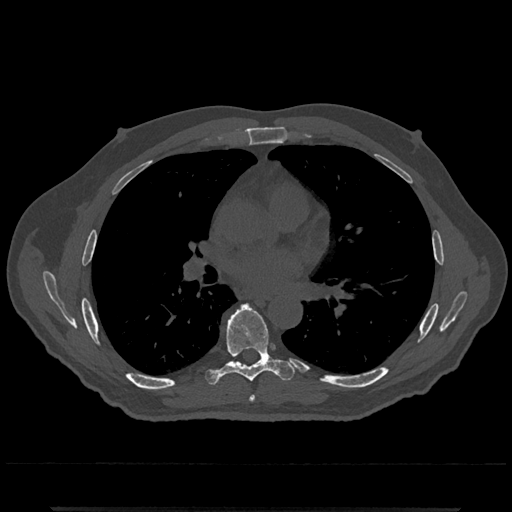
CT including the spine, one axial slice. Position 724 of 797 along the scan axis. 120 kVp. Bone window (W 1800 / L 400 HU). 512 × 512 image matrix, field of view 393 × 393 mm. Male patient, age 67 years. From the clinical record (not read from this slice): primary cancer: prostate.
Outlined on this slice (semi-automatic segmentation, software-assisted and operator-edited):
- T6 vertebra: box from (x=249, y=395) to (x=256, y=402) px
- T7 vertebra: (x=206, y=304)–(x=295, y=385)